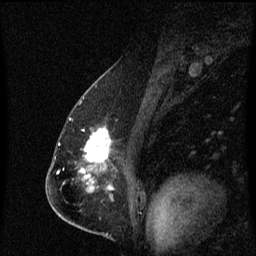
Breast MRI (dynamic contrast-enhanced), one sagittal slice; slice 39 of 60 in the series (ordered by position); dynamic contrast-enhanced series, image 2 of 3 at this slice position (ordered by acquisition); 1.5 T; TE 4.2 ms, TR 8.4 ms; 256 × 256 image matrix. Patient: female, 57 years. From the clinical record (not read from this slice): setting: breast cancer imaged before/during neoadjuvant chemotherapy; receptor status: HR-positive, HER2-negative.
Structures marked on this image (semi-automatically segmented with operator editing):
- analysis volume of interest (the breast-tissue region the enhancement analysis was run in; not a lesion): bounding box <76,128,111,177> (left, top, right, bottom; pixels)
- tumour enhancement mask (voxels above the 70 % enhancement threshold inside the analysis volume of interest): <80,128,111,177>